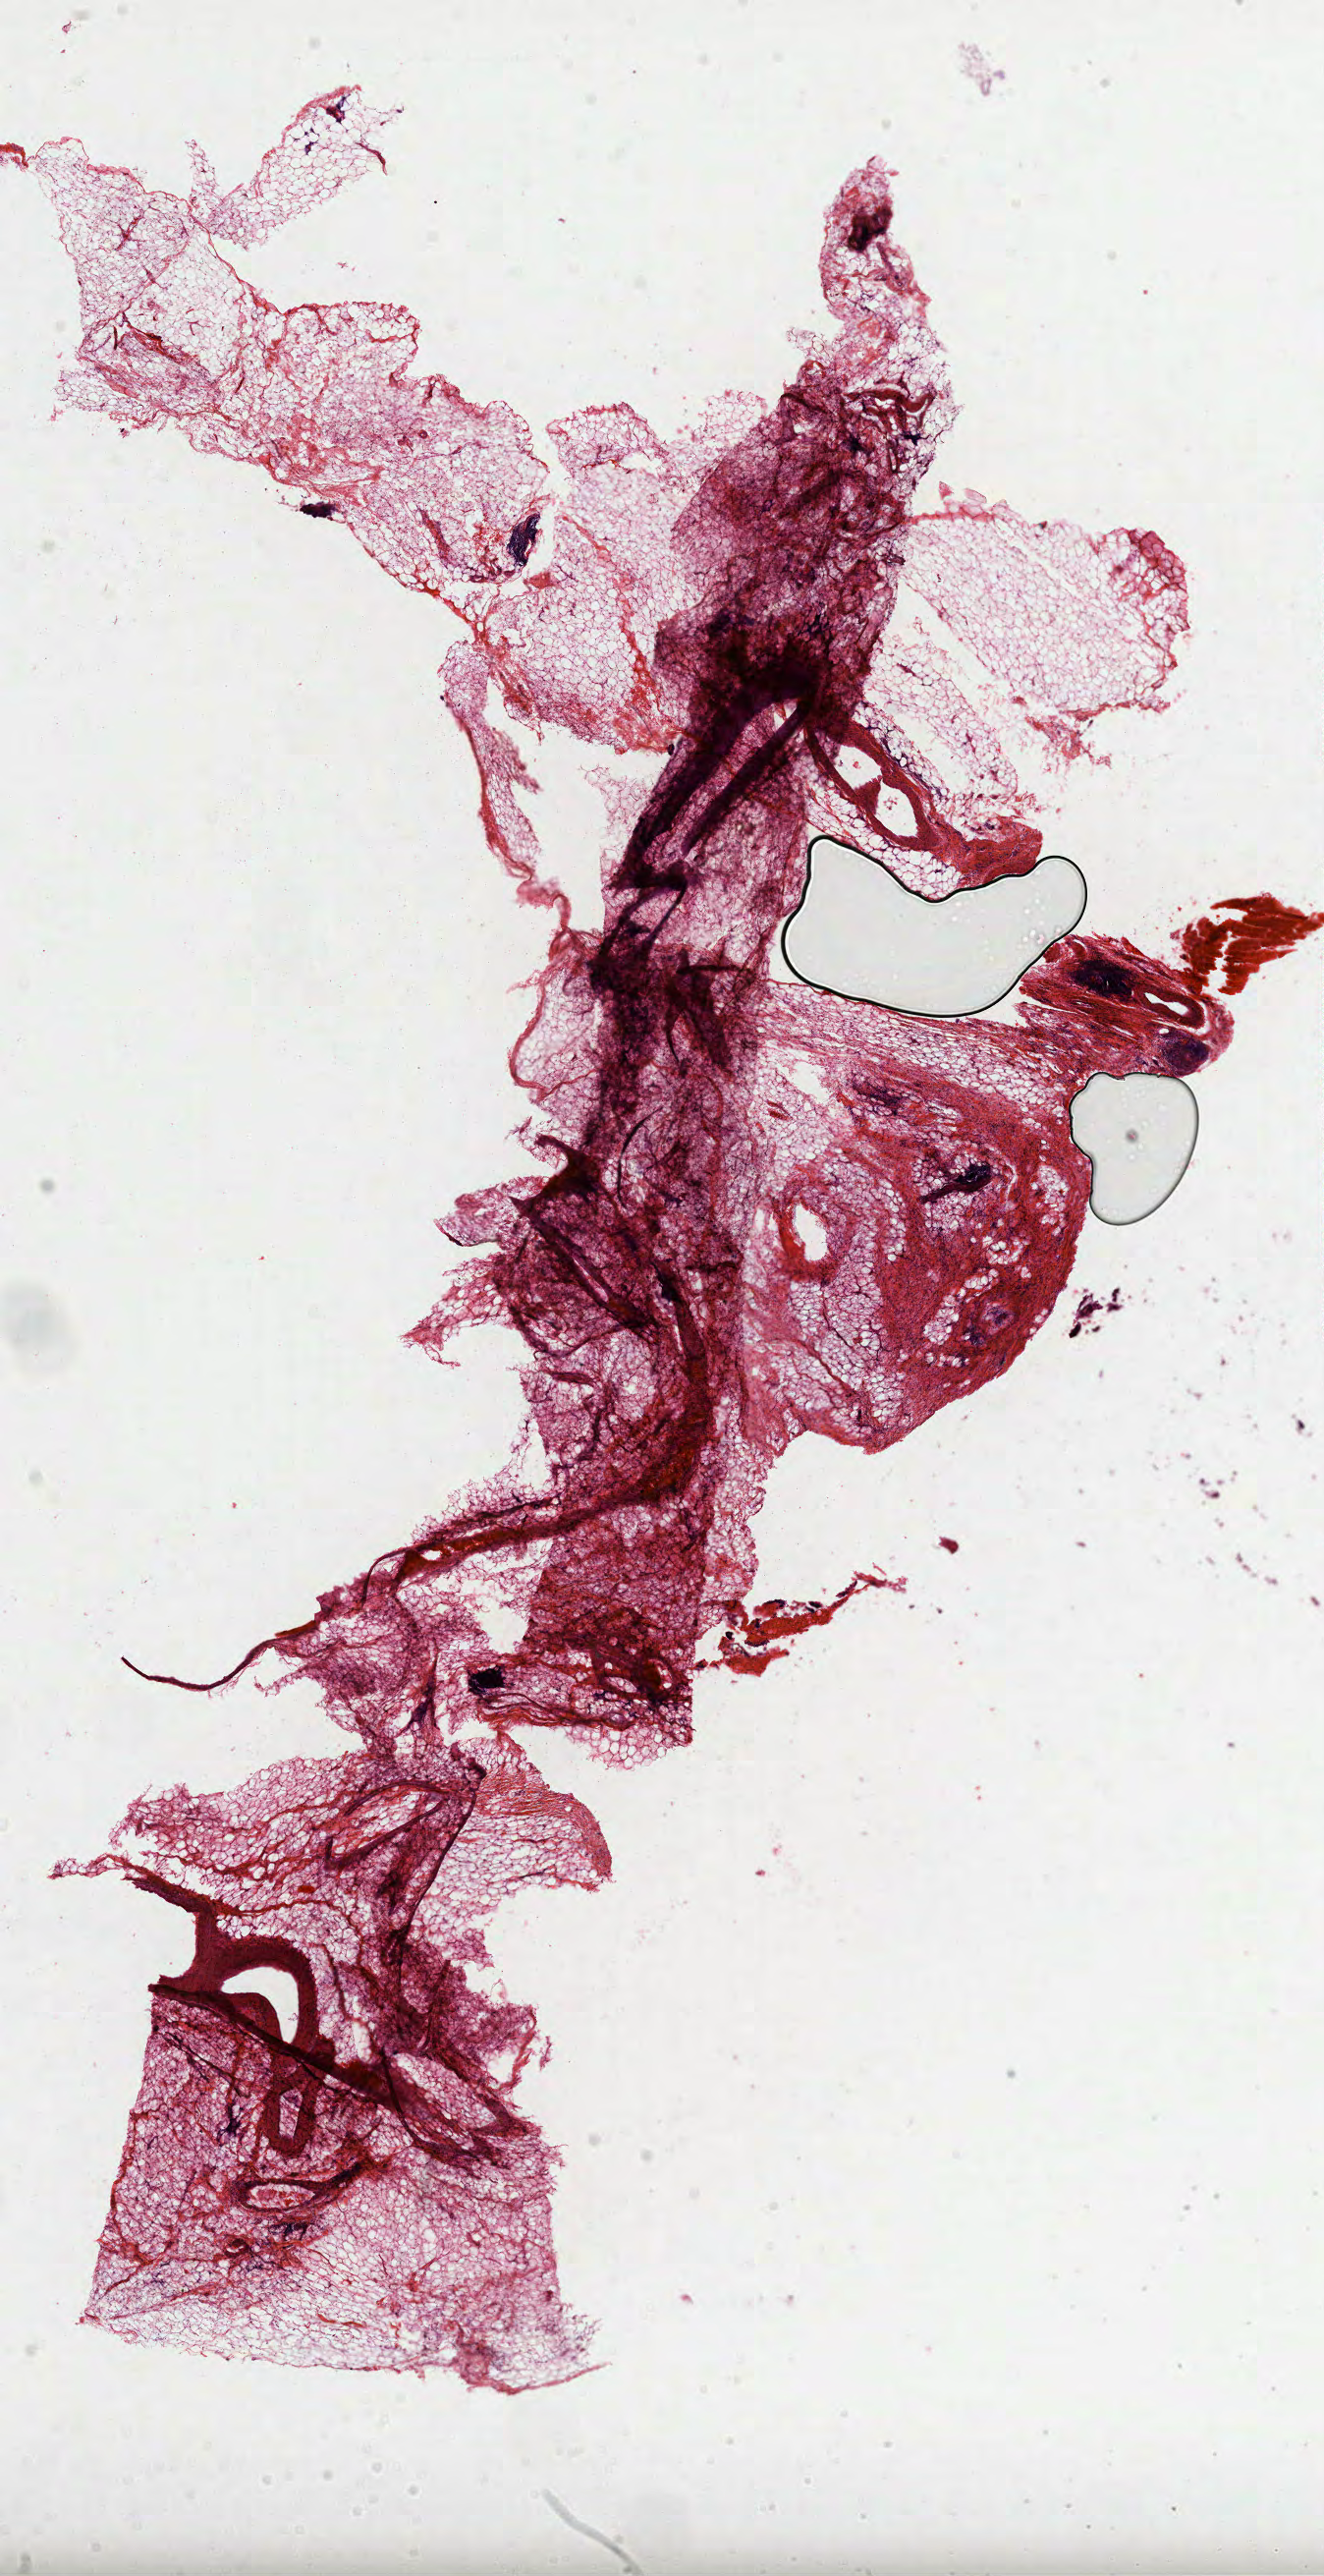
Hematoxylin and eosin (H&E) stained whole-slide image — a low-resolution overview of the entire scanned area, about 10.9 x 21.2 mm (slide scanned at 40x). Formalin-fixed paraffin-embedded (FFPE) diagnostic section. Sample: primary tumour, colon. Female, age 77 years at initial diagnosis.
* AJCC pathologic stage: IIA (5th edition)
* lymph nodes positive (case pathology): 0 of 18 examined
* pathologic diagnosis: Adenocarcinoma, NOS (sigmoid colon)